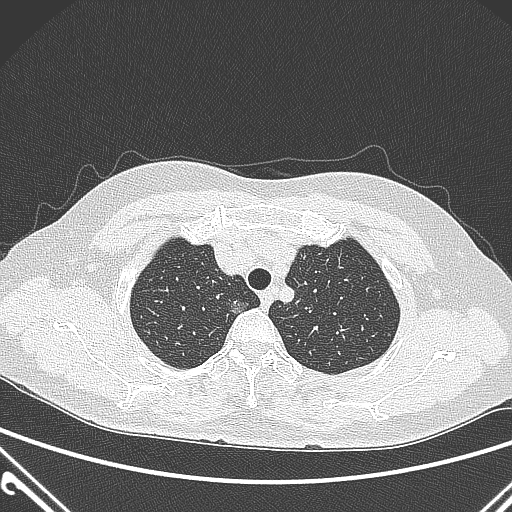
Chest CT, one axial slice. Slice 237 of 300 in the series (ordered by position). Lung window (W 1500 / L -600 HU). 1 mm slice thickness. 512 × 512 image matrix, field of view 350 × 350 mm. Patient: female, 54 years. Case-level facts recorded for this patient, not image findings: clinical TNM (as recorded): T1a N0 M0.
Outlined on this slice (rectangle marked by the reading radiologist):
- lung tumour (recorded histology: adenocarcinoma): bounding box (x1, y1, x2, y2) in pixels: (226, 294, 257, 327)